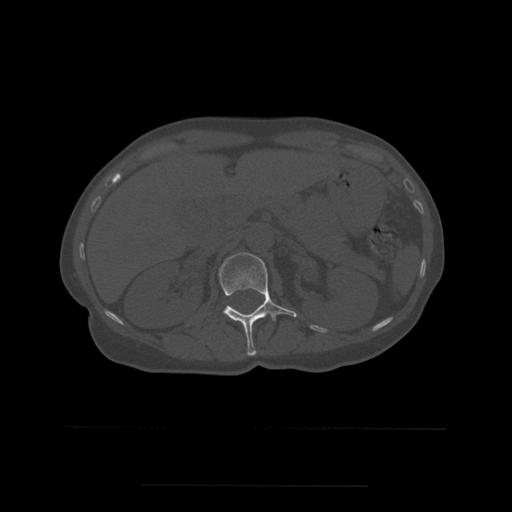
CT including the spine, one axial slice; position 234 of 544 along the scan axis; bone window (W 1800 / L 400 HU); 512 × 512 image matrix, field of view 350 × 350 mm. Patient age 58 years. From the clinical record (not read from this slice): primary cancer: lung.
Outlined on this slice (semi-automatically segmented with operator editing):
- L1 vertebra: box from (x=219, y=253) to (x=297, y=356) px